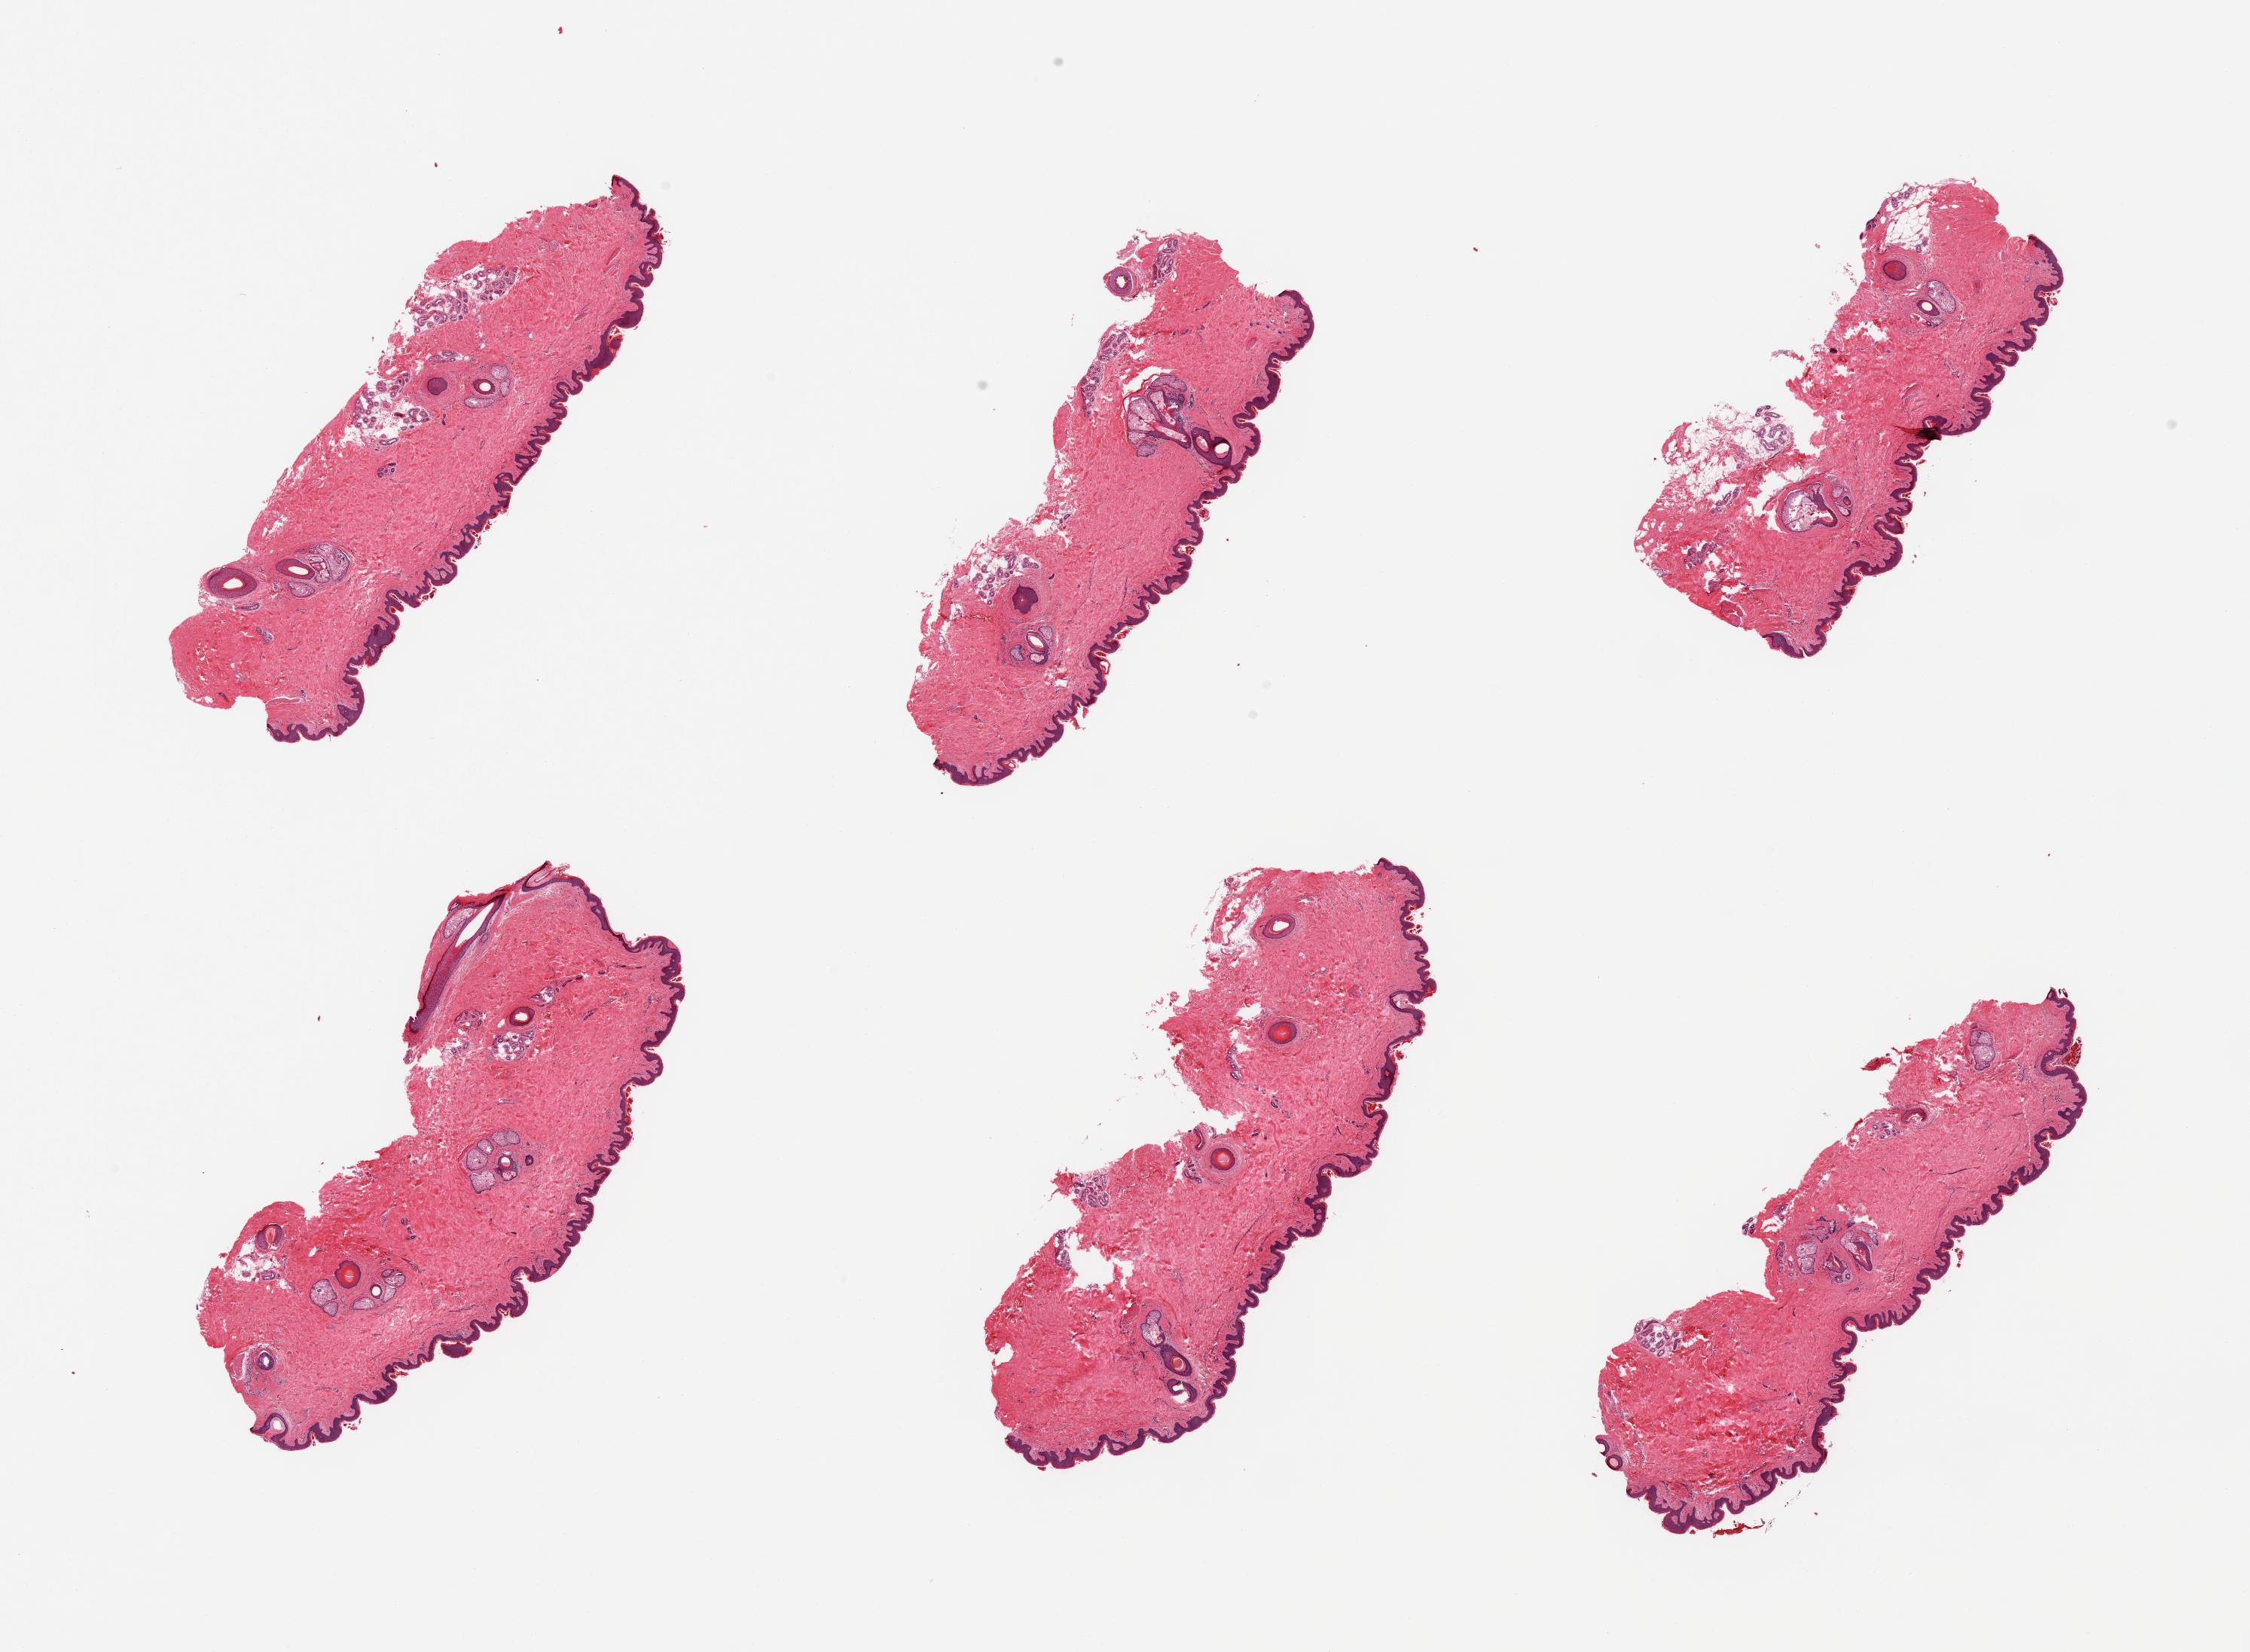
Hematoxylin and eosin (H&E) whole-slide image, a low-resolution overview of the entire scanned area, about 23.6 x 17.3 mm; PAXgene-fixed, paraffin-embedded tissue; target tissue: skin of suprapubic region; donor tissue sample. Donor sex: male.
Pathologist's review note for this sample: 6 pieces; prominent hair follicles; 5% dermal fat; small foci of benign keratosis; well trimmed.